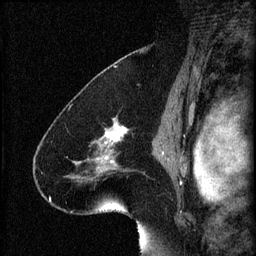
Breast MRI (dynamic contrast-enhanced), one sagittal slice. Slice 43 of 60 in the series (ordered by position). 3 images stored at this slice position (order not interpretable as contrast timing). 1.5 T. TE 4.2 ms, TR 8.2 ms. 256 × 256 image matrix, field of view 180 × 180 mm. Patient: female, 41 years.
Annotated regions visible in this slice (semi-automatic segmentation, software-assisted and operator-edited):
- analysis volume of interest (the breast-tissue region the enhancement analysis was run in; not a lesion): box from (x=72, y=120) to (x=134, y=183) px
- tumour enhancement mask (voxels above the 70 % enhancement threshold inside the analysis volume of interest): (x=75, y=122)–(x=128, y=173)